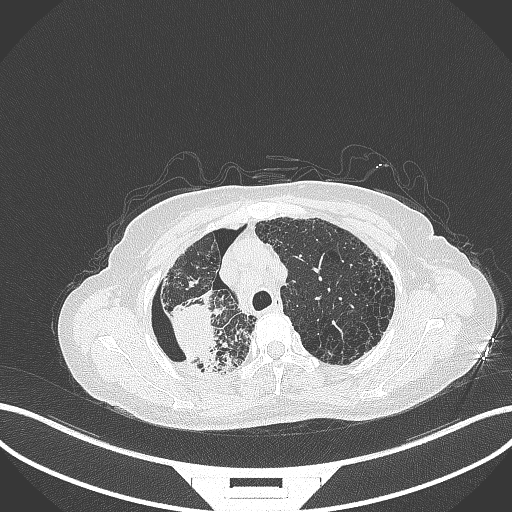
Chest CT, one axial slice. Slice 277 of 408 in the series (ordered by position). 120 kVp. Lung window (W 1500 / L -600 HU). 1 mm slice thickness. 512 × 512 image matrix. Patient: female, 64 years. Case-level facts recorded for this patient, not image findings: clinical TNM (as recorded): T3 N3 M0.
Structures marked on this image (rectangle marked by the reading radiologist):
- lung tumour (recorded histology: squamous cell carcinoma): box from (x=169, y=303) to (x=222, y=364) px